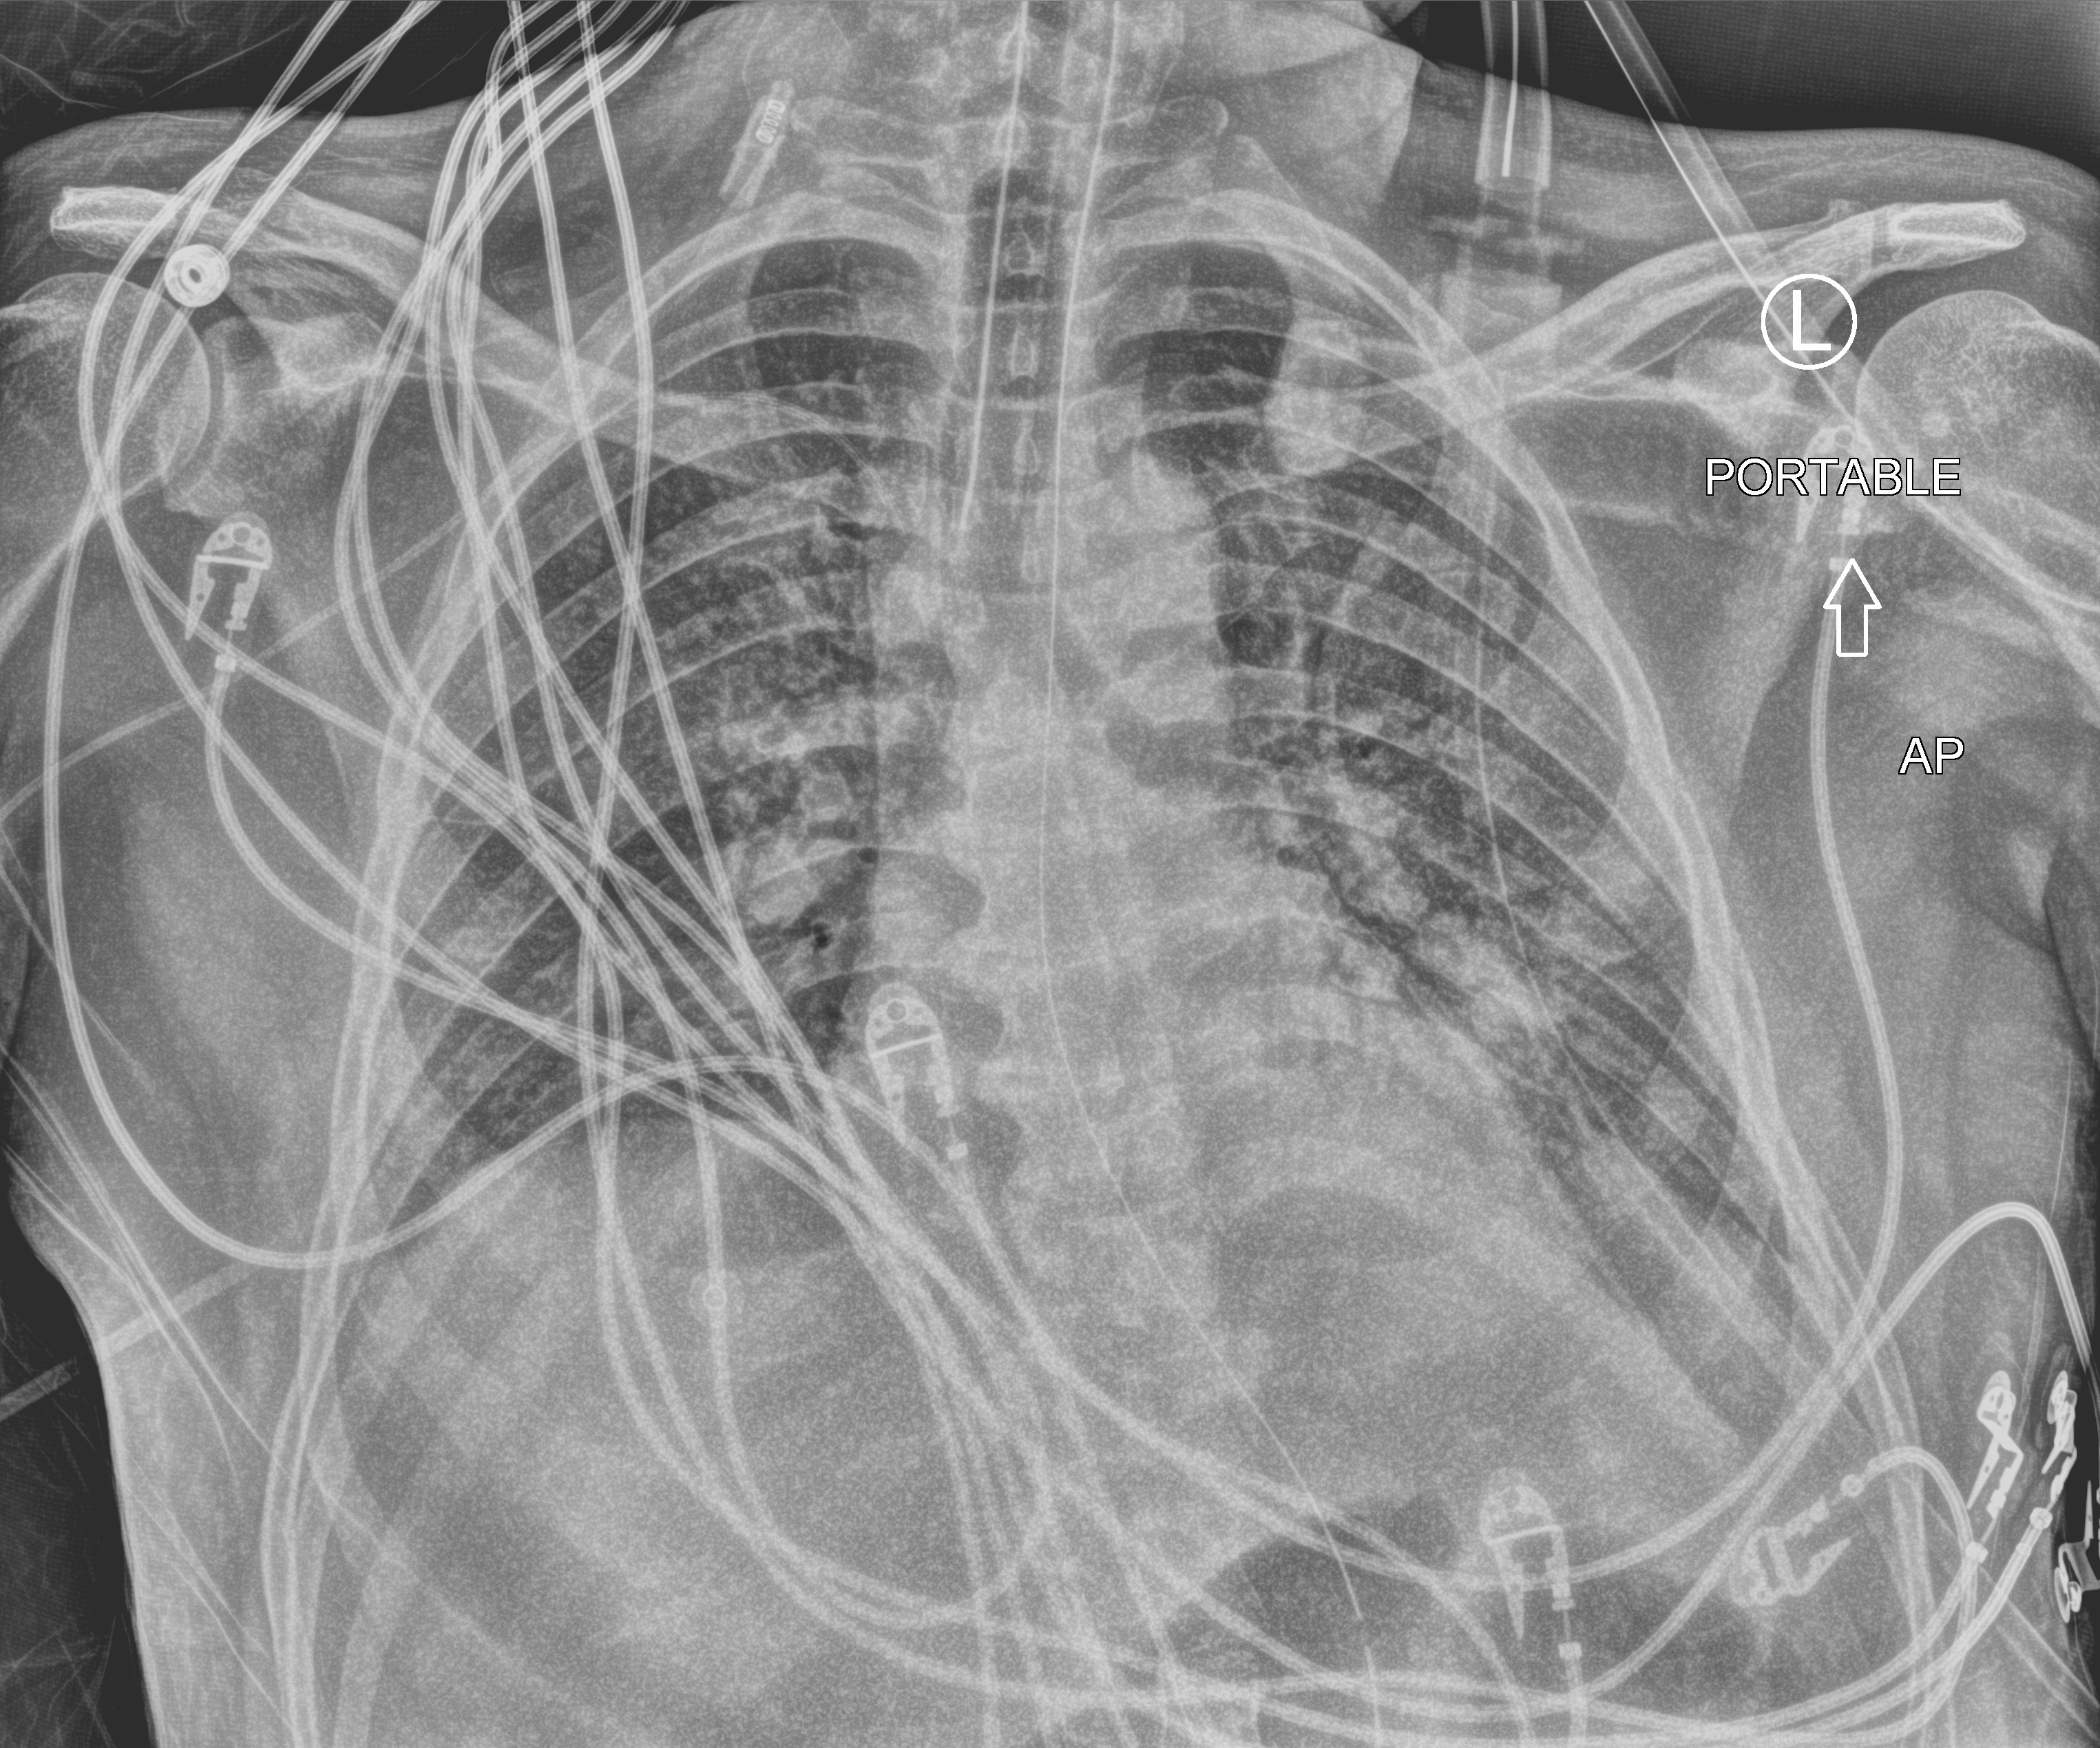
Bedside chest radiograph (computed radiography); anteroposterior (AP) projection. Patient hospitalised with COVID-19; male, aged 18–59 years.
From the hospital-stay record, not from the radiograph (when in the stay this image was taken is not recorded): mechanically ventilated during this hospital stay: yes.